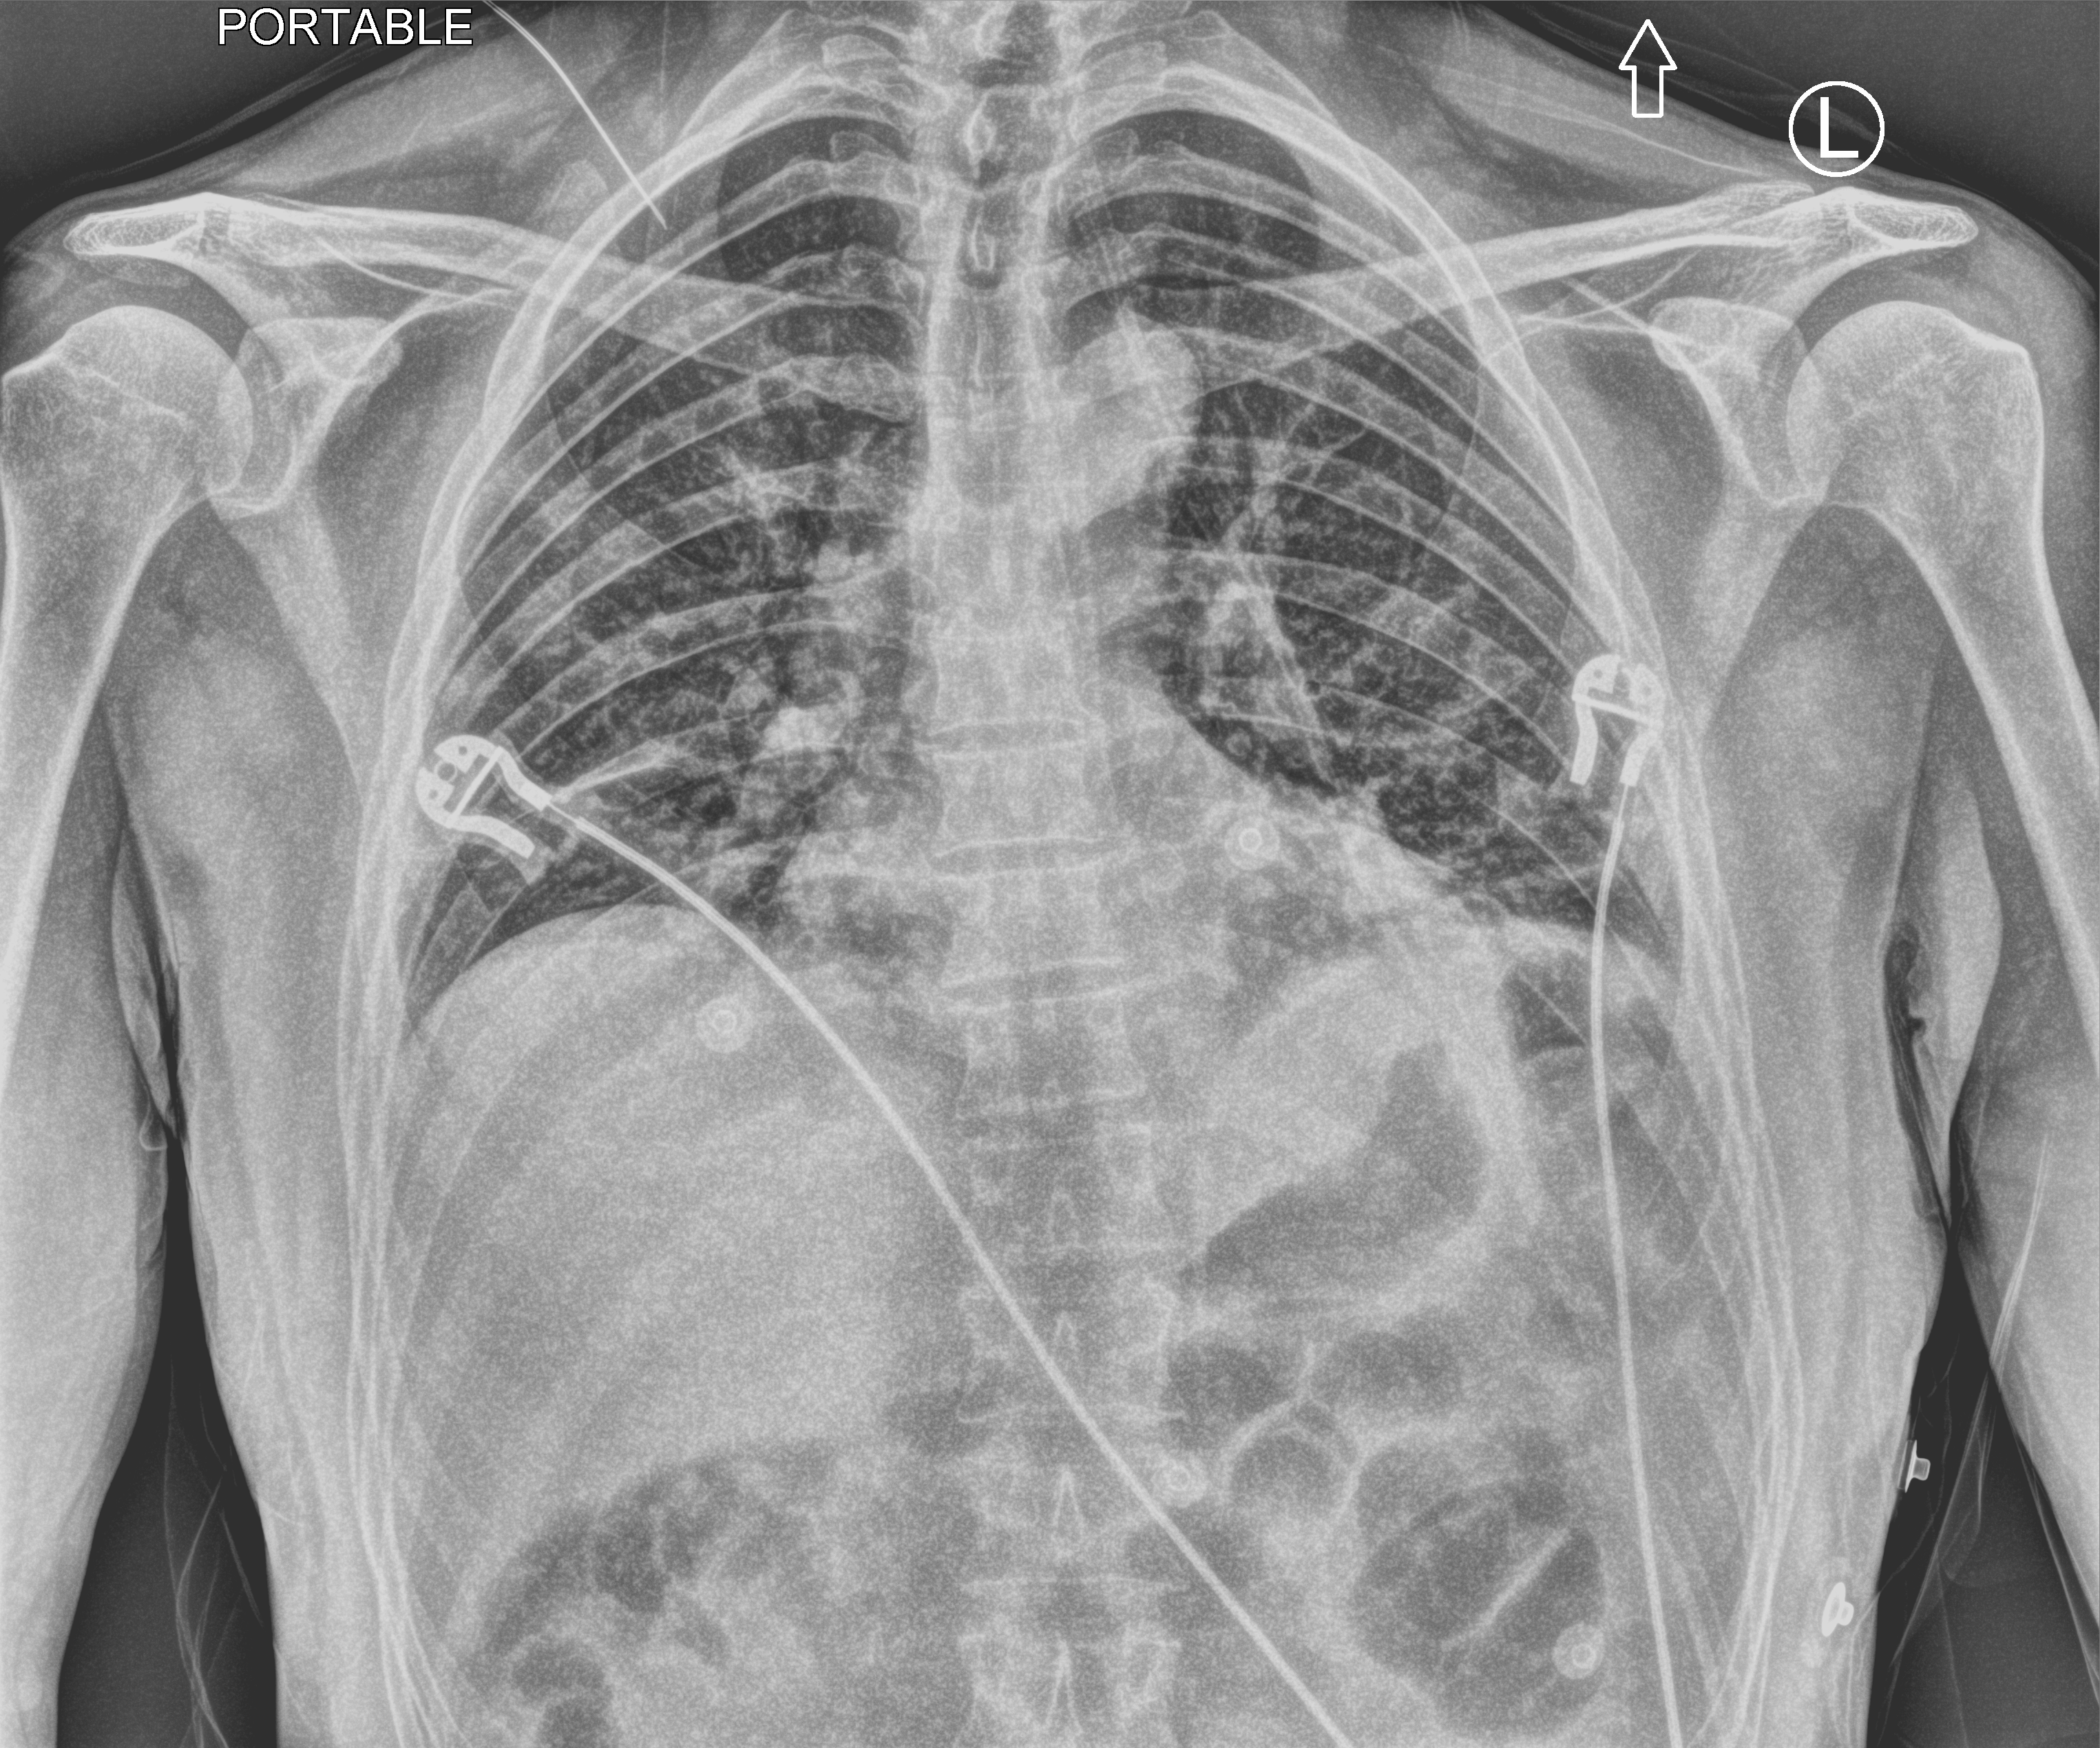
Portable chest radiograph. Male patient hospitalised with COVID-19, age 18–59 years.
Hospital-stay facts (about this admission, not read from this image; timing relative to this image not recorded):
- chronic kidney disease (admission record): no
- admitted to intensive care during this hospital stay: no